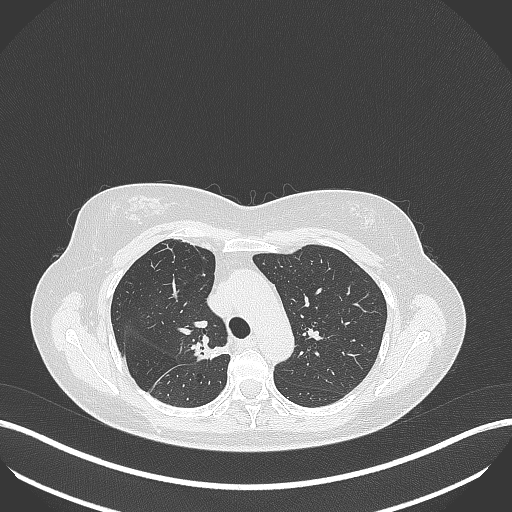
Chest CT, one axial slice. Slice 279 of 386 in the series (ordered by position). Reconstruction kernel B70f. 120 kVp. Lung window (W 1500 / L -600 HU). 1 mm slice thickness. 512 × 512 image matrix, field of view 400 × 400 mm. Patient: female, 65 years. Case-level facts recorded for this patient, not image findings: clinical TNM (as recorded): T1b N0 M0.
Outlined on this slice (bounding box drawn by a radiologist):
- lung tumour (recorded histology: adenocarcinoma): bounding box [x1, y1, x2, y2] px = [188, 339, 231, 361]